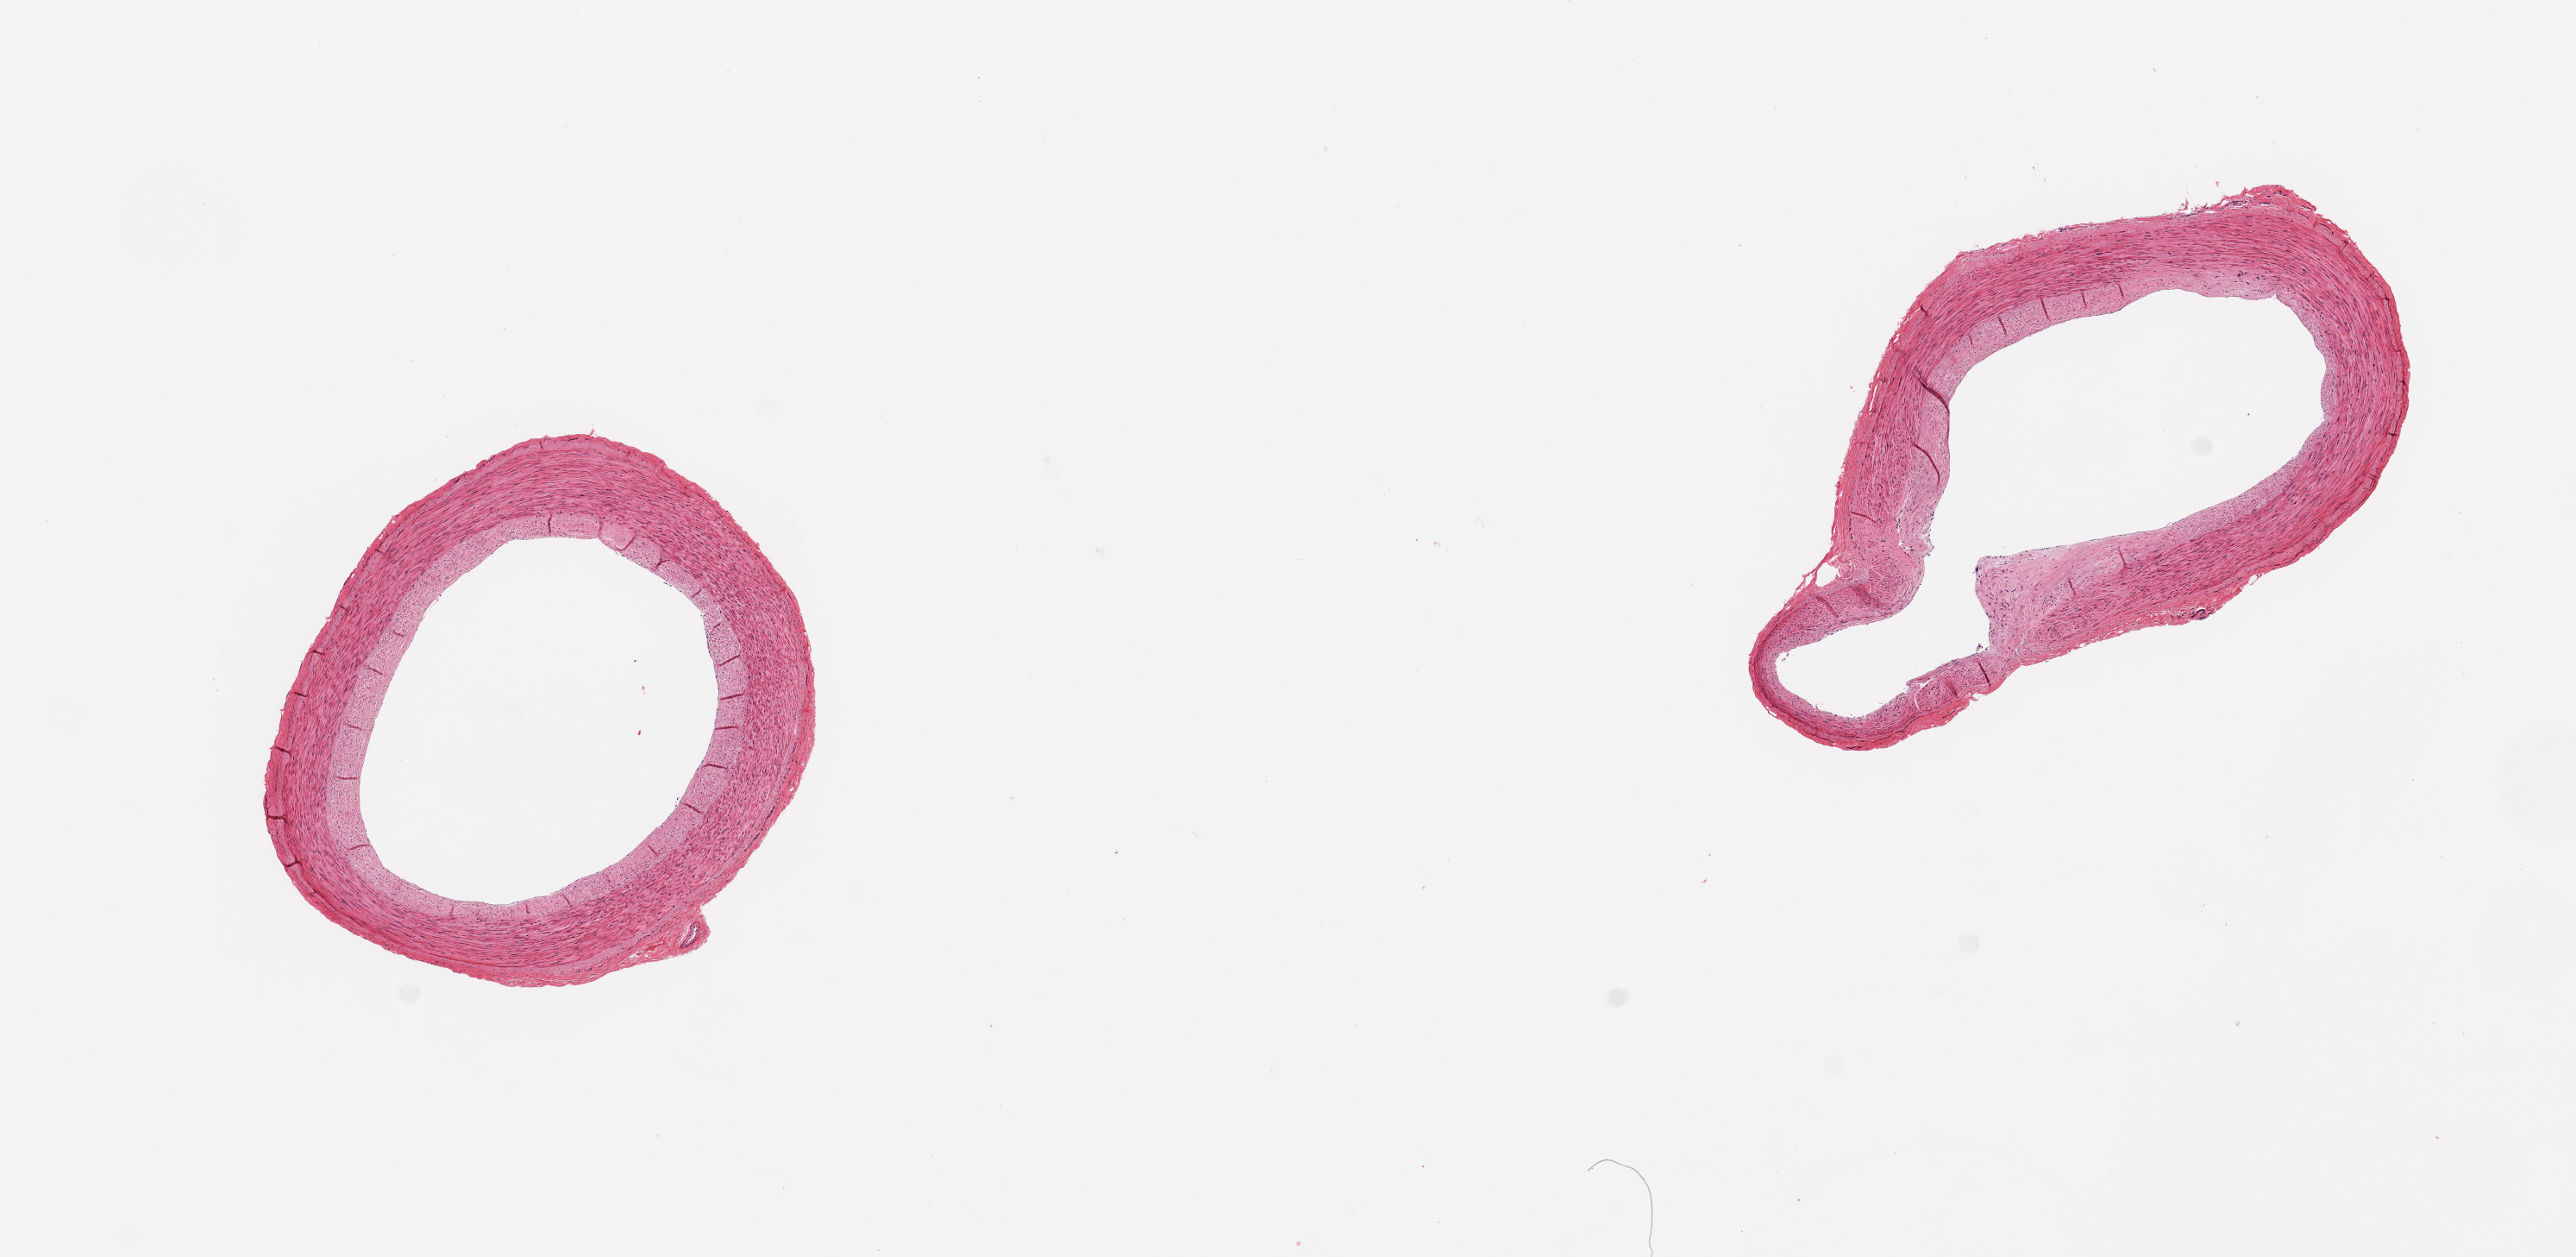
Digitized haematoxylin and eosin-stained section, whole scanned area (about 11.8 x 5.8 mm, acquisition: 20x scan) shown as a low-resolution overview. PAXgene-fixed paraffin-embedded (PFPE) section. Section of tibial artery (target tissue). Donor tissue sample. Donor sex: male.
Review note (as recorded): 2 pieces; well trimmed artery with focal atheromatous plaque.